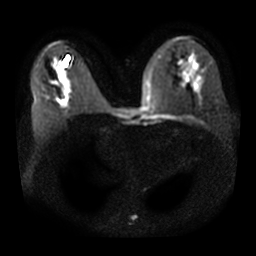
Breast MRI, one axial slice; position 15 of 31 along the scan axis; diffusion-weighted series; image 2 of 4 stored at this slice position (different b-values; order by instance number); 3 T; 256 × 256 image matrix. Female patient.
Annotated regions visible in this slice (manually delineated by an expert):
- tumour on diffusion-weighted imaging: box from (x=61, y=102) to (x=64, y=104) px